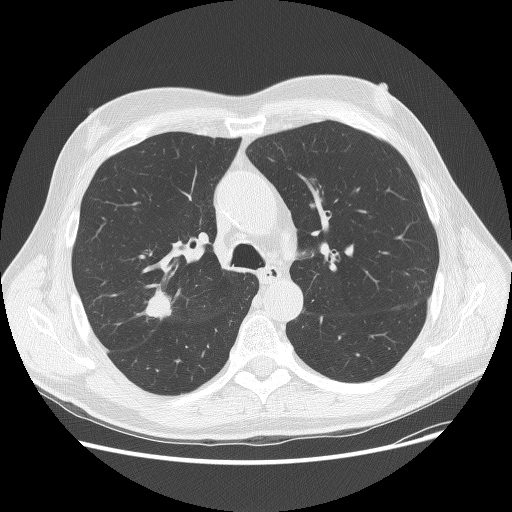
Chest CT (low-dose screening protocol), one axial image; first (baseline) screen; lung window (W 1500 / L -600 HU); lung (sharp) reconstruction kernel (BONE); 120 kVp; slice 53 of 156 in the series. Male participant, aged 70 years at enrolment.
Lesion marked by an expert reader, bounding box <133,280,195,335> (left, top, right, bottom; pixels). The screening reader recorded 2 non-calcified nodules or masses ≥4 mm on this exam (right upper lobe, left lower lobe); which of them this box marks is not recorded. Later outcome: lung cancer diagnosed 15 days after this screen — adenocarcinoma, NOS, right upper lobe, poorly differentiated (G3), stage IIA (AJCC 6th edition), 23 mm at pathology.